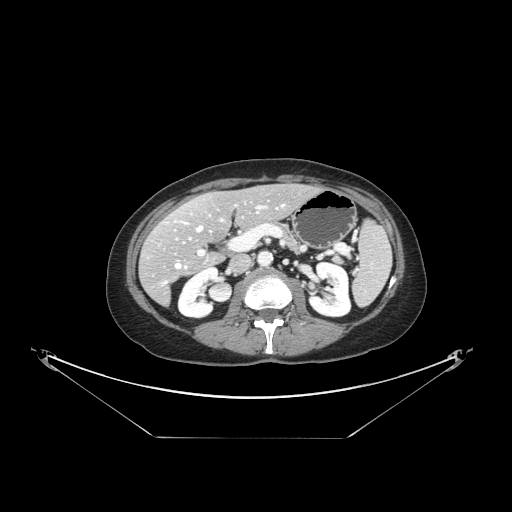
Contrast-enhanced abdominal CT, one axial slice. Slice 72 of 148 in the series (ordered by position). Intravenous contrast given. Soft-tissue window (W 400 / L 40 HU). 512 × 512 image matrix, field of view 500 × 500 mm. Female patient, age 73 years. Case-level facts recorded for this patient, not image findings: diagnosis: colorectal cancer liver metastases, imaged before liver resection; multiple liver metastases: no.
Outlined on this slice (manually delineated by an expert):
- hepatic veins: bounding box (x1, y1, x2, y2) in pixels: (162, 205, 284, 285)
- liver: (140, 186, 315, 303)
- planned liver remnant (the part of the liver to remain after resection): (168, 185, 315, 246)
- portal vein (with intrahepatic branches): (198, 206, 263, 255)